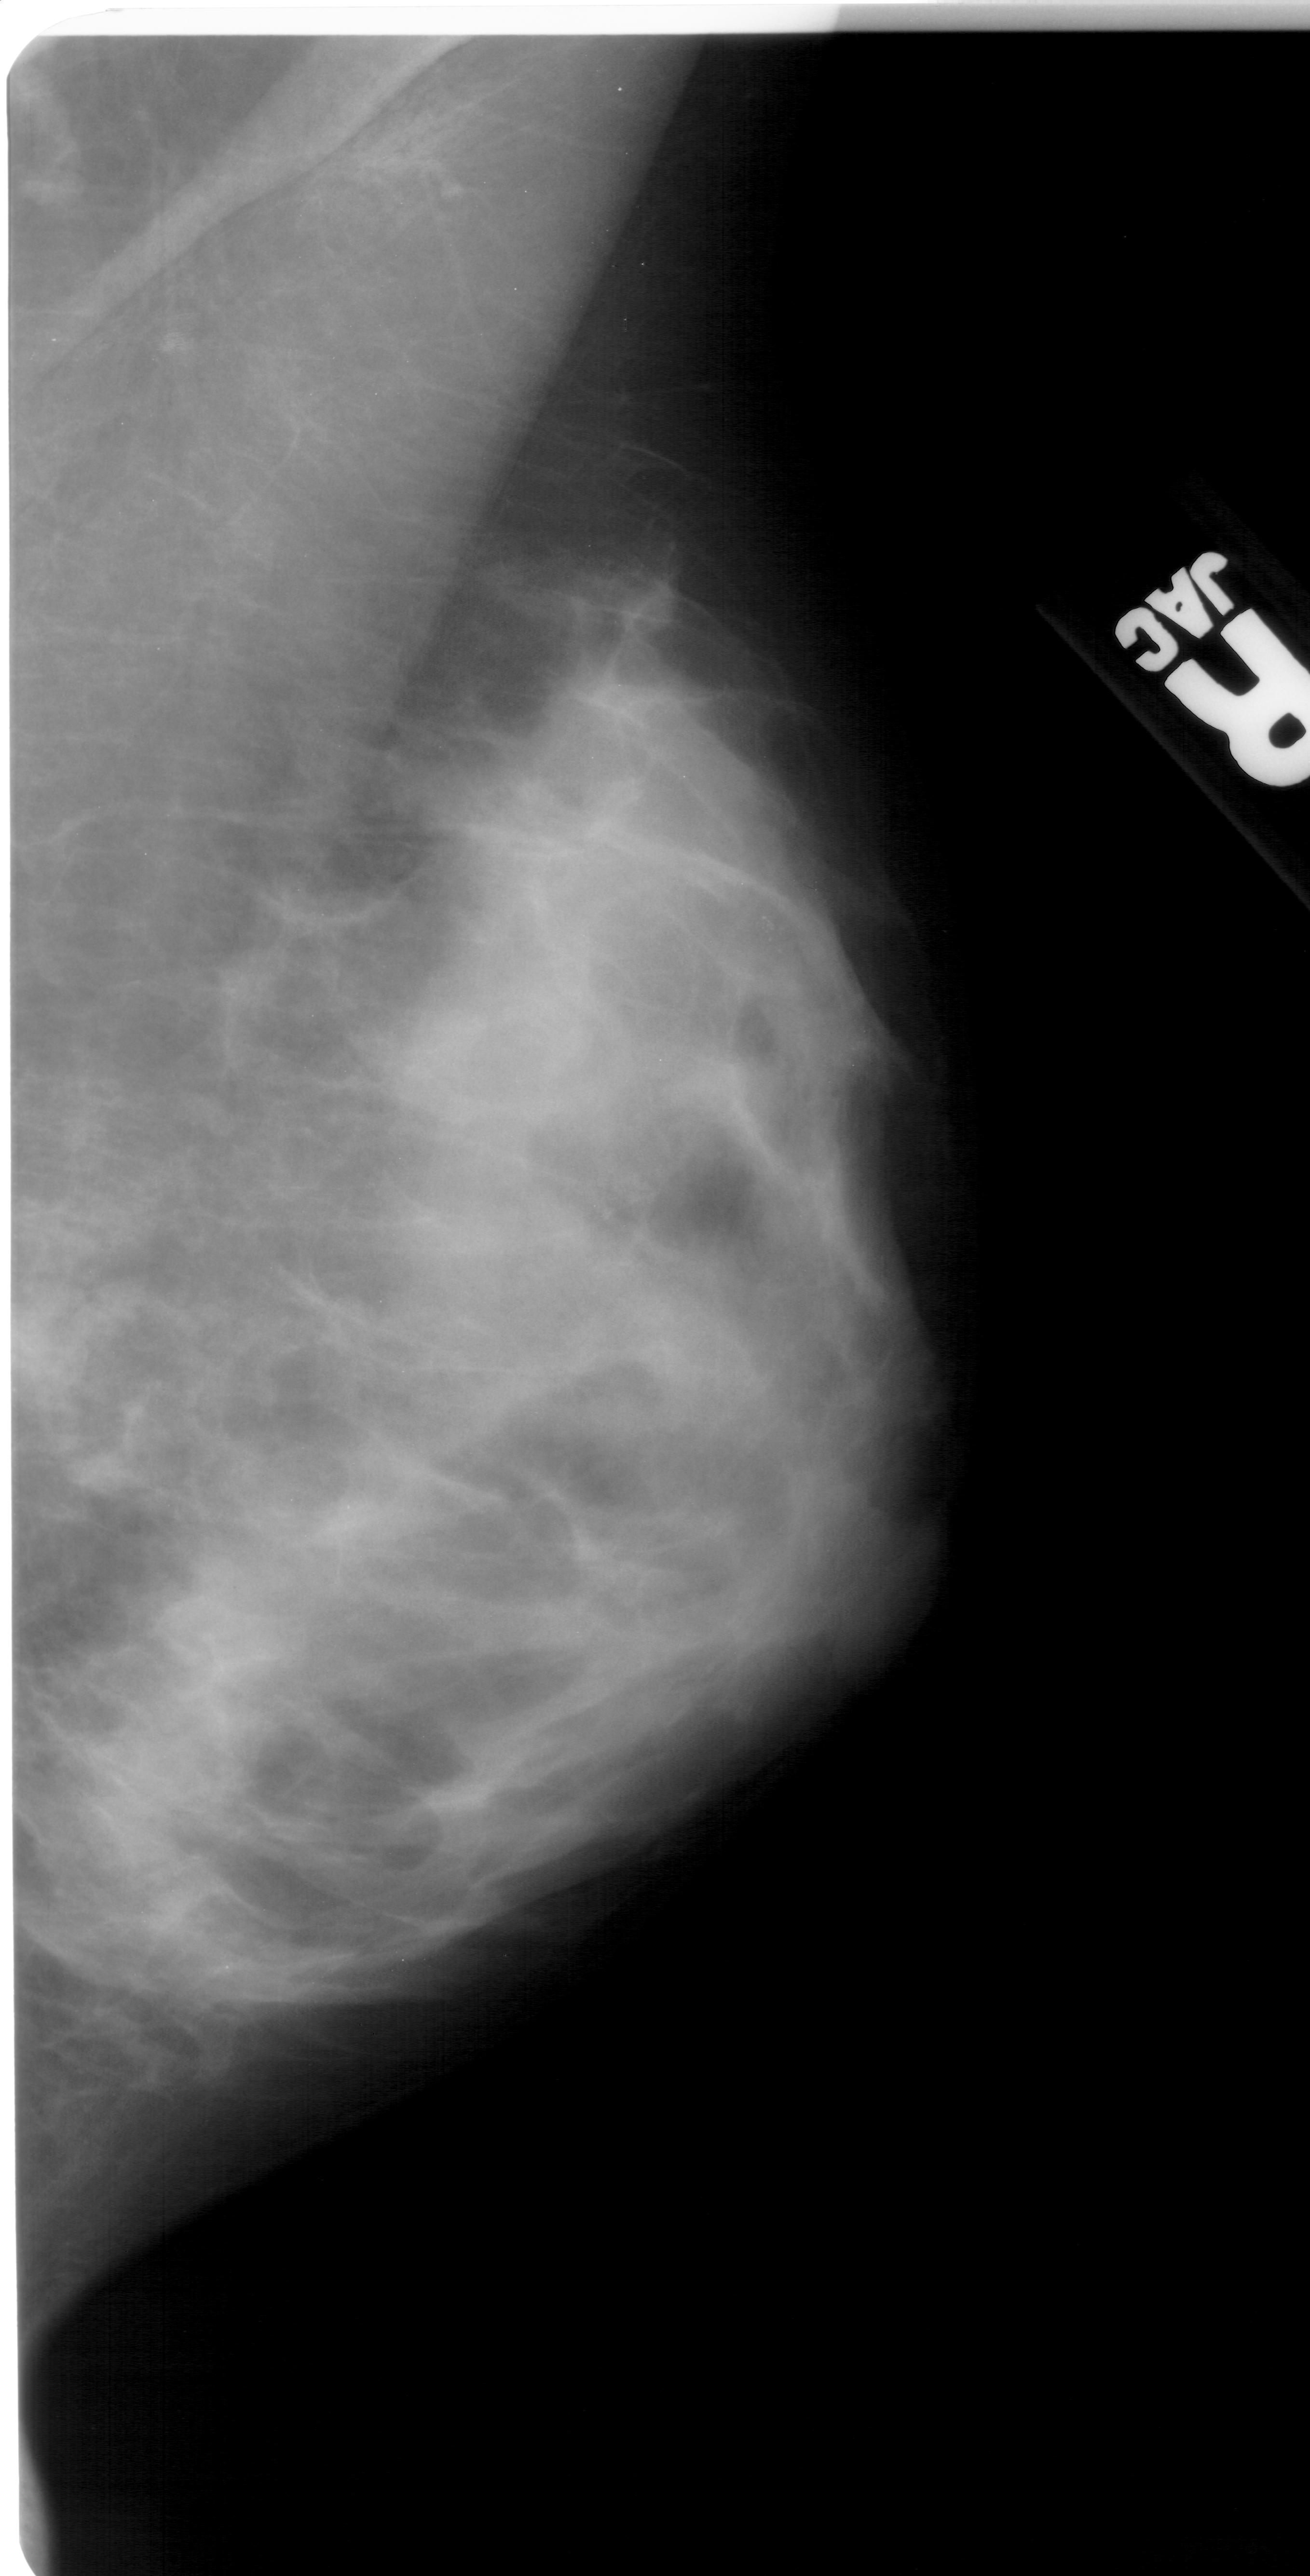
Scanned film-screen mammogram; right breast; MLO view; BI-RADS breast density category 4 (scale 1–4); 1310 × 2576 image matrix.
Marked abnormalities (boxes around the expert regions of interest):
- calcifications, morphology pleomorphic, distribution clustered; BI-RADS assessment category 4; subtlety rating 4 on a 1 (subtle) to 5 (obvious) scale; pathology (as recorded): benign: box from (x=719, y=854) to (x=875, y=1022) px